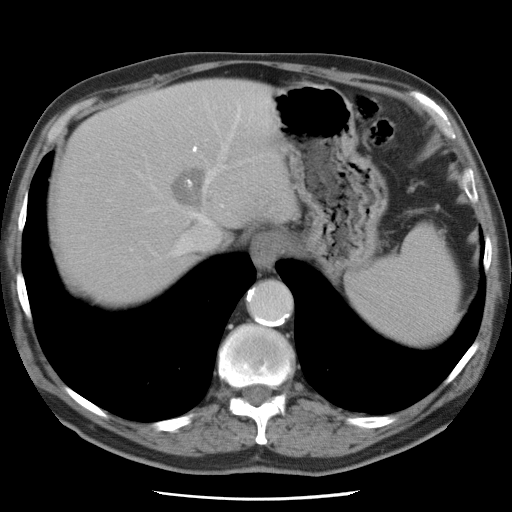
Contrast-enhanced abdominal CT, one axial slice. Position 64 of 78 along the scan axis. 120 kVp. Intravenous contrast given. Soft-tissue window (W 400 / L 40 HU). 5 mm slice thickness. 512 × 512 image matrix, field of view 337 × 337 mm. Male patient, age 75 years. From the clinical record (not read from this slice): diagnosis: colorectal cancer liver metastases, imaged before liver resection; multiple liver metastases: yes; largest metastasis: 2.4 cm; disease in both lobes: yes.
Annotated regions visible in this slice (outlined manually by an expert reader):
- hepatic veins: bounding box <172,102,262,256> (left, top, right, bottom; pixels)
- liver: <56,80,296,304>
- planned liver remnant (the part of the liver to remain after resection): <56,137,193,304>
- liver metastasis: <170,168,207,208>